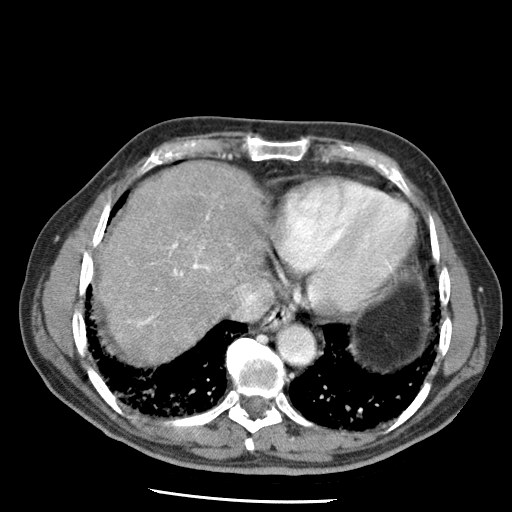
Contrast-enhanced abdominal CT (liver protocol), one axial slice. Slice 58 of 79 in the series (ordered by position). 120 kVp. Soft-tissue window (W 400 / L 40 HU). 2.5 mm slice thickness. 512 × 512 image matrix, field of view 320 × 320 mm. Case-level facts recorded for this patient, not image findings: diagnosis: hepatocellular carcinoma (patient treated with transarterial chemoembolisation; whether this scan precedes or follows treatment is not stated here); TNM stage (as recorded): Stage-IIIA; Child-Pugh class: A.
Structures marked on this image (semi-automatic segmentation, software-assisted and operator-edited):
- abdominal aorta: bounding box (x1, y1, x2, y2) in pixels: (277, 325, 314, 362)
- liver parenchyma outside the tumour (the mass and vessels are separate outlines, so this box may not span the whole liver): (98, 162, 266, 362)
- liver vessels: (127, 214, 240, 327)